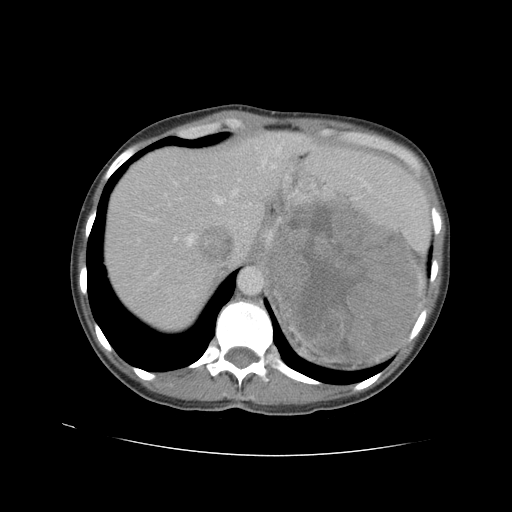
Contrast-enhanced abdominal CT, one axial slice; position 76 of 90 along the scan axis; reconstruction kernel STANDARD; intravenous contrast given; soft-tissue window (W 400 / L 40 HU); 5 mm slice thickness; 512 × 512 image matrix, field of view 360 × 360 mm. Female patient. From the clinical record (not read from this slice): diagnosis: adrenocortical carcinoma; tumour side: left adrenal; tumour size at pathology: 18 cm; Ki-67 index: 11 %.
Annotated regions visible in this slice (semi-automatic segmentation, software-assisted and operator-edited):
- mass: box from (x=270, y=201) to (x=416, y=361) px